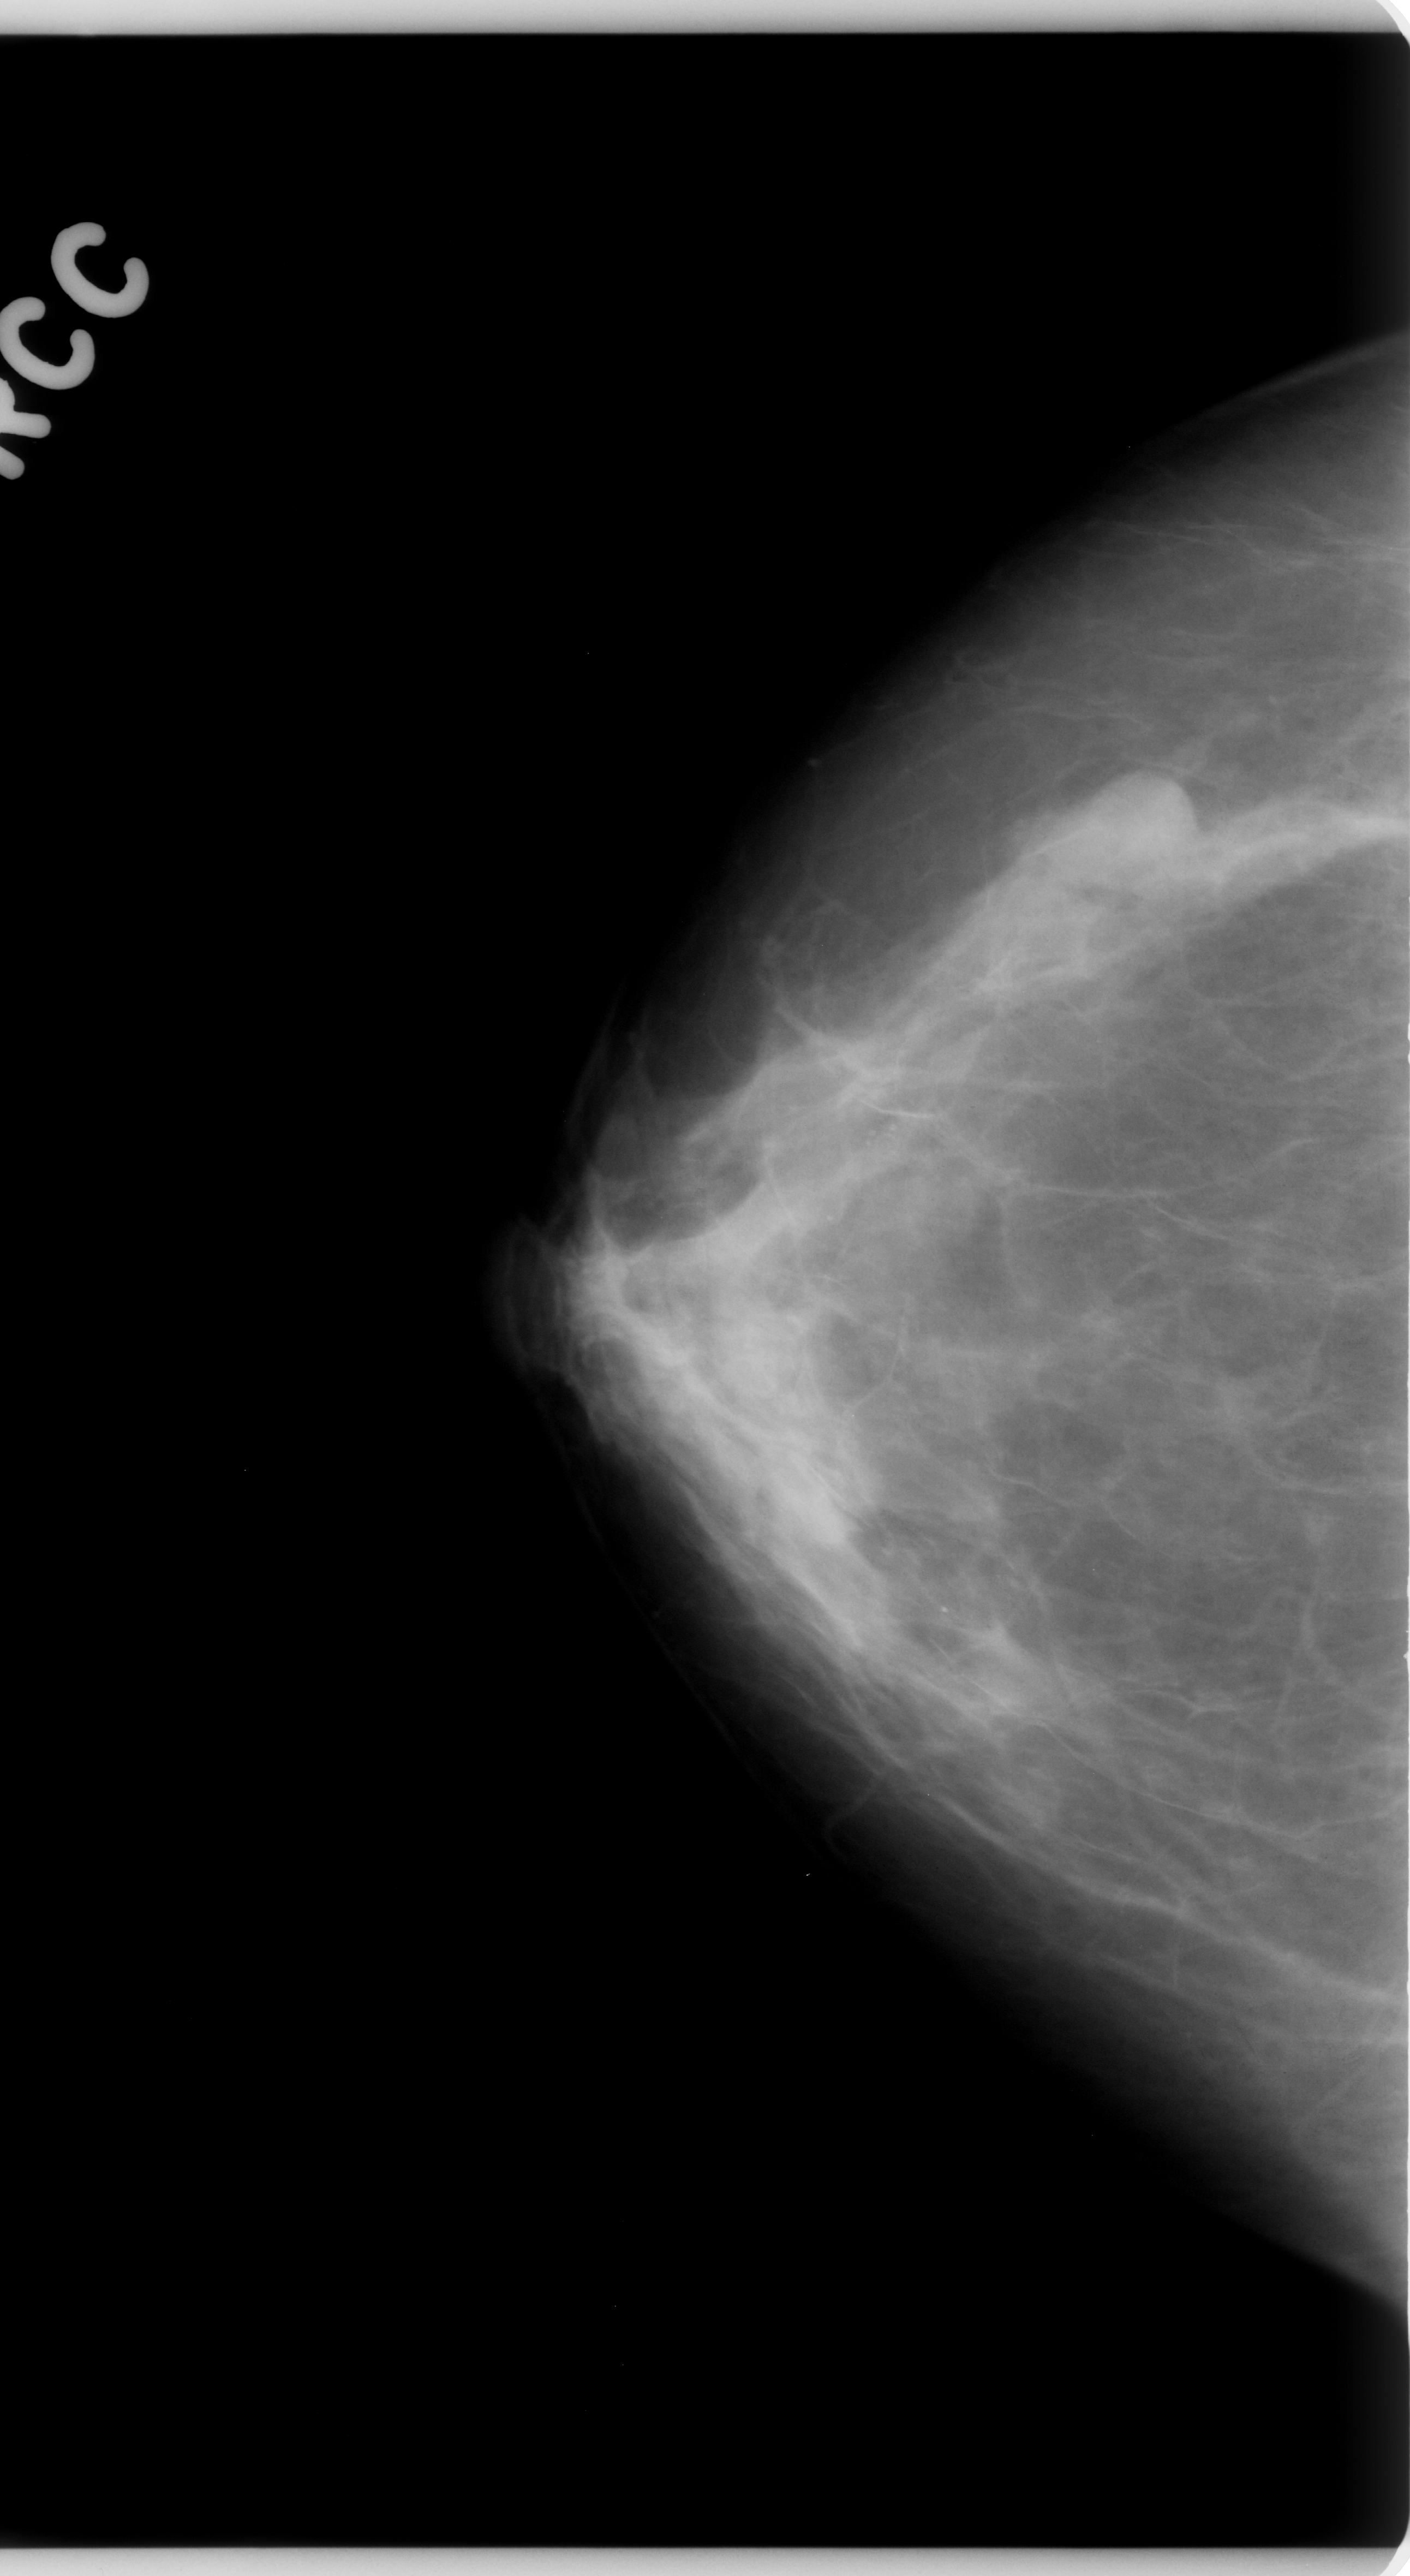
Digitized screen-film mammogram. Right breast. CC view. Breast composition: scattered fibroglandular densities (BI-RADS density category 2 of 4). 1410 × 2576 image matrix.
Expert-marked regions of interest on this image (one box per marked abnormality):
- mass, shape oval, margins circumscribed; BI-RADS assessment category 4; pathology (as recorded): benign: bounding box [x1, y1, x2, y2] px = [1033, 757, 1200, 903]